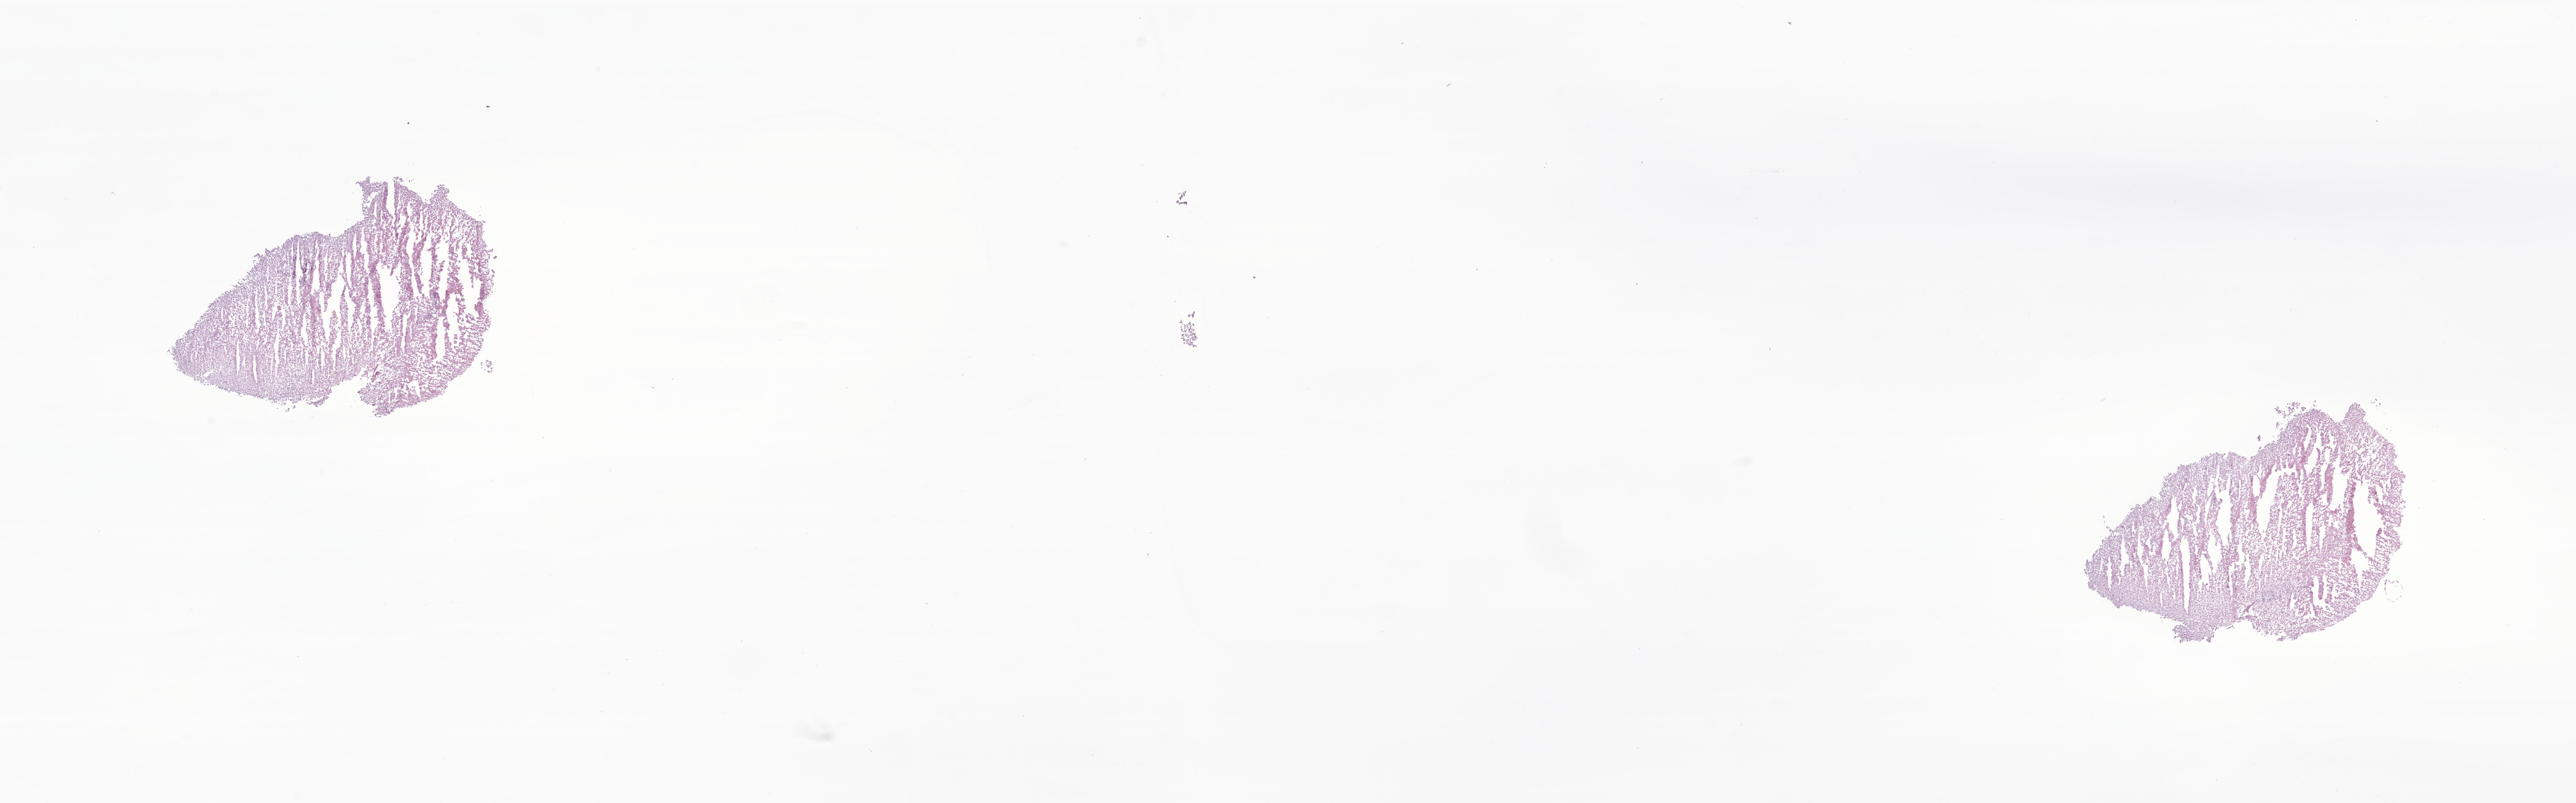
Digitized haematoxylin and eosin-stained section of tumor tissue from the parietal lobe, whole scanned area (about 29.5 x 9.2 mm) shown as a low-resolution overview; frozen section. Male patient, age 161 months (13 years 5 months).
- diagnosis: Glioma, malignant